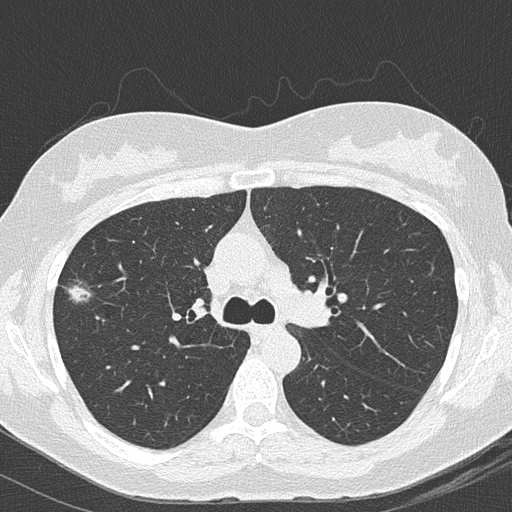
Chest CT (low-dose screening protocol), one axial image. Second annual screen. Lung window (W 1500 / L -600 HU). 2 mm slice thickness. Female participant, aged 64 years at enrolment.
• Expert reader's lesion annotation, bounding box (x1, y1, x2, y2) in pixels: (48, 265, 105, 316).
• Reader record for this screening exam (exam-level; its link to the box is not recorded): non-calcified nodule or mass ≥4 mm, right upper lobe, 16 × 13 mm, mixed attenuation, pre-existing on the prior screen: yes; interval growth: yes.
• Participant outcome: lung cancer diagnosed 112 days after this screen — bronchiolo-alveolar adenocarcinoma, NOS, right upper lobe, well differentiated (G1), stage IA (AJCC 6th edition), 10 mm at pathology.